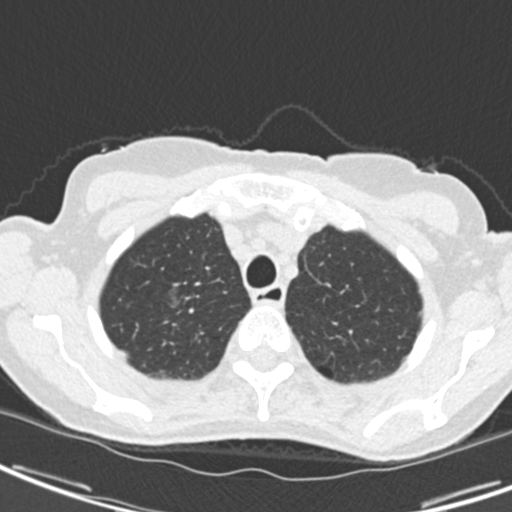
Low-dose screening chest CT, one axial slice; slice 166 of 189 in the series (ordered by position); reconstruction kernel B30f; lung window (W 1500 / L -600 HU); 2 mm slice thickness; 512 × 512 image matrix, field of view 279 × 279 mm.
Structures marked on this image (manually delineated by an expert):
- lesion 1 (tumor, upper lobe of right lung): box from (x=170, y=288) to (x=183, y=308) px